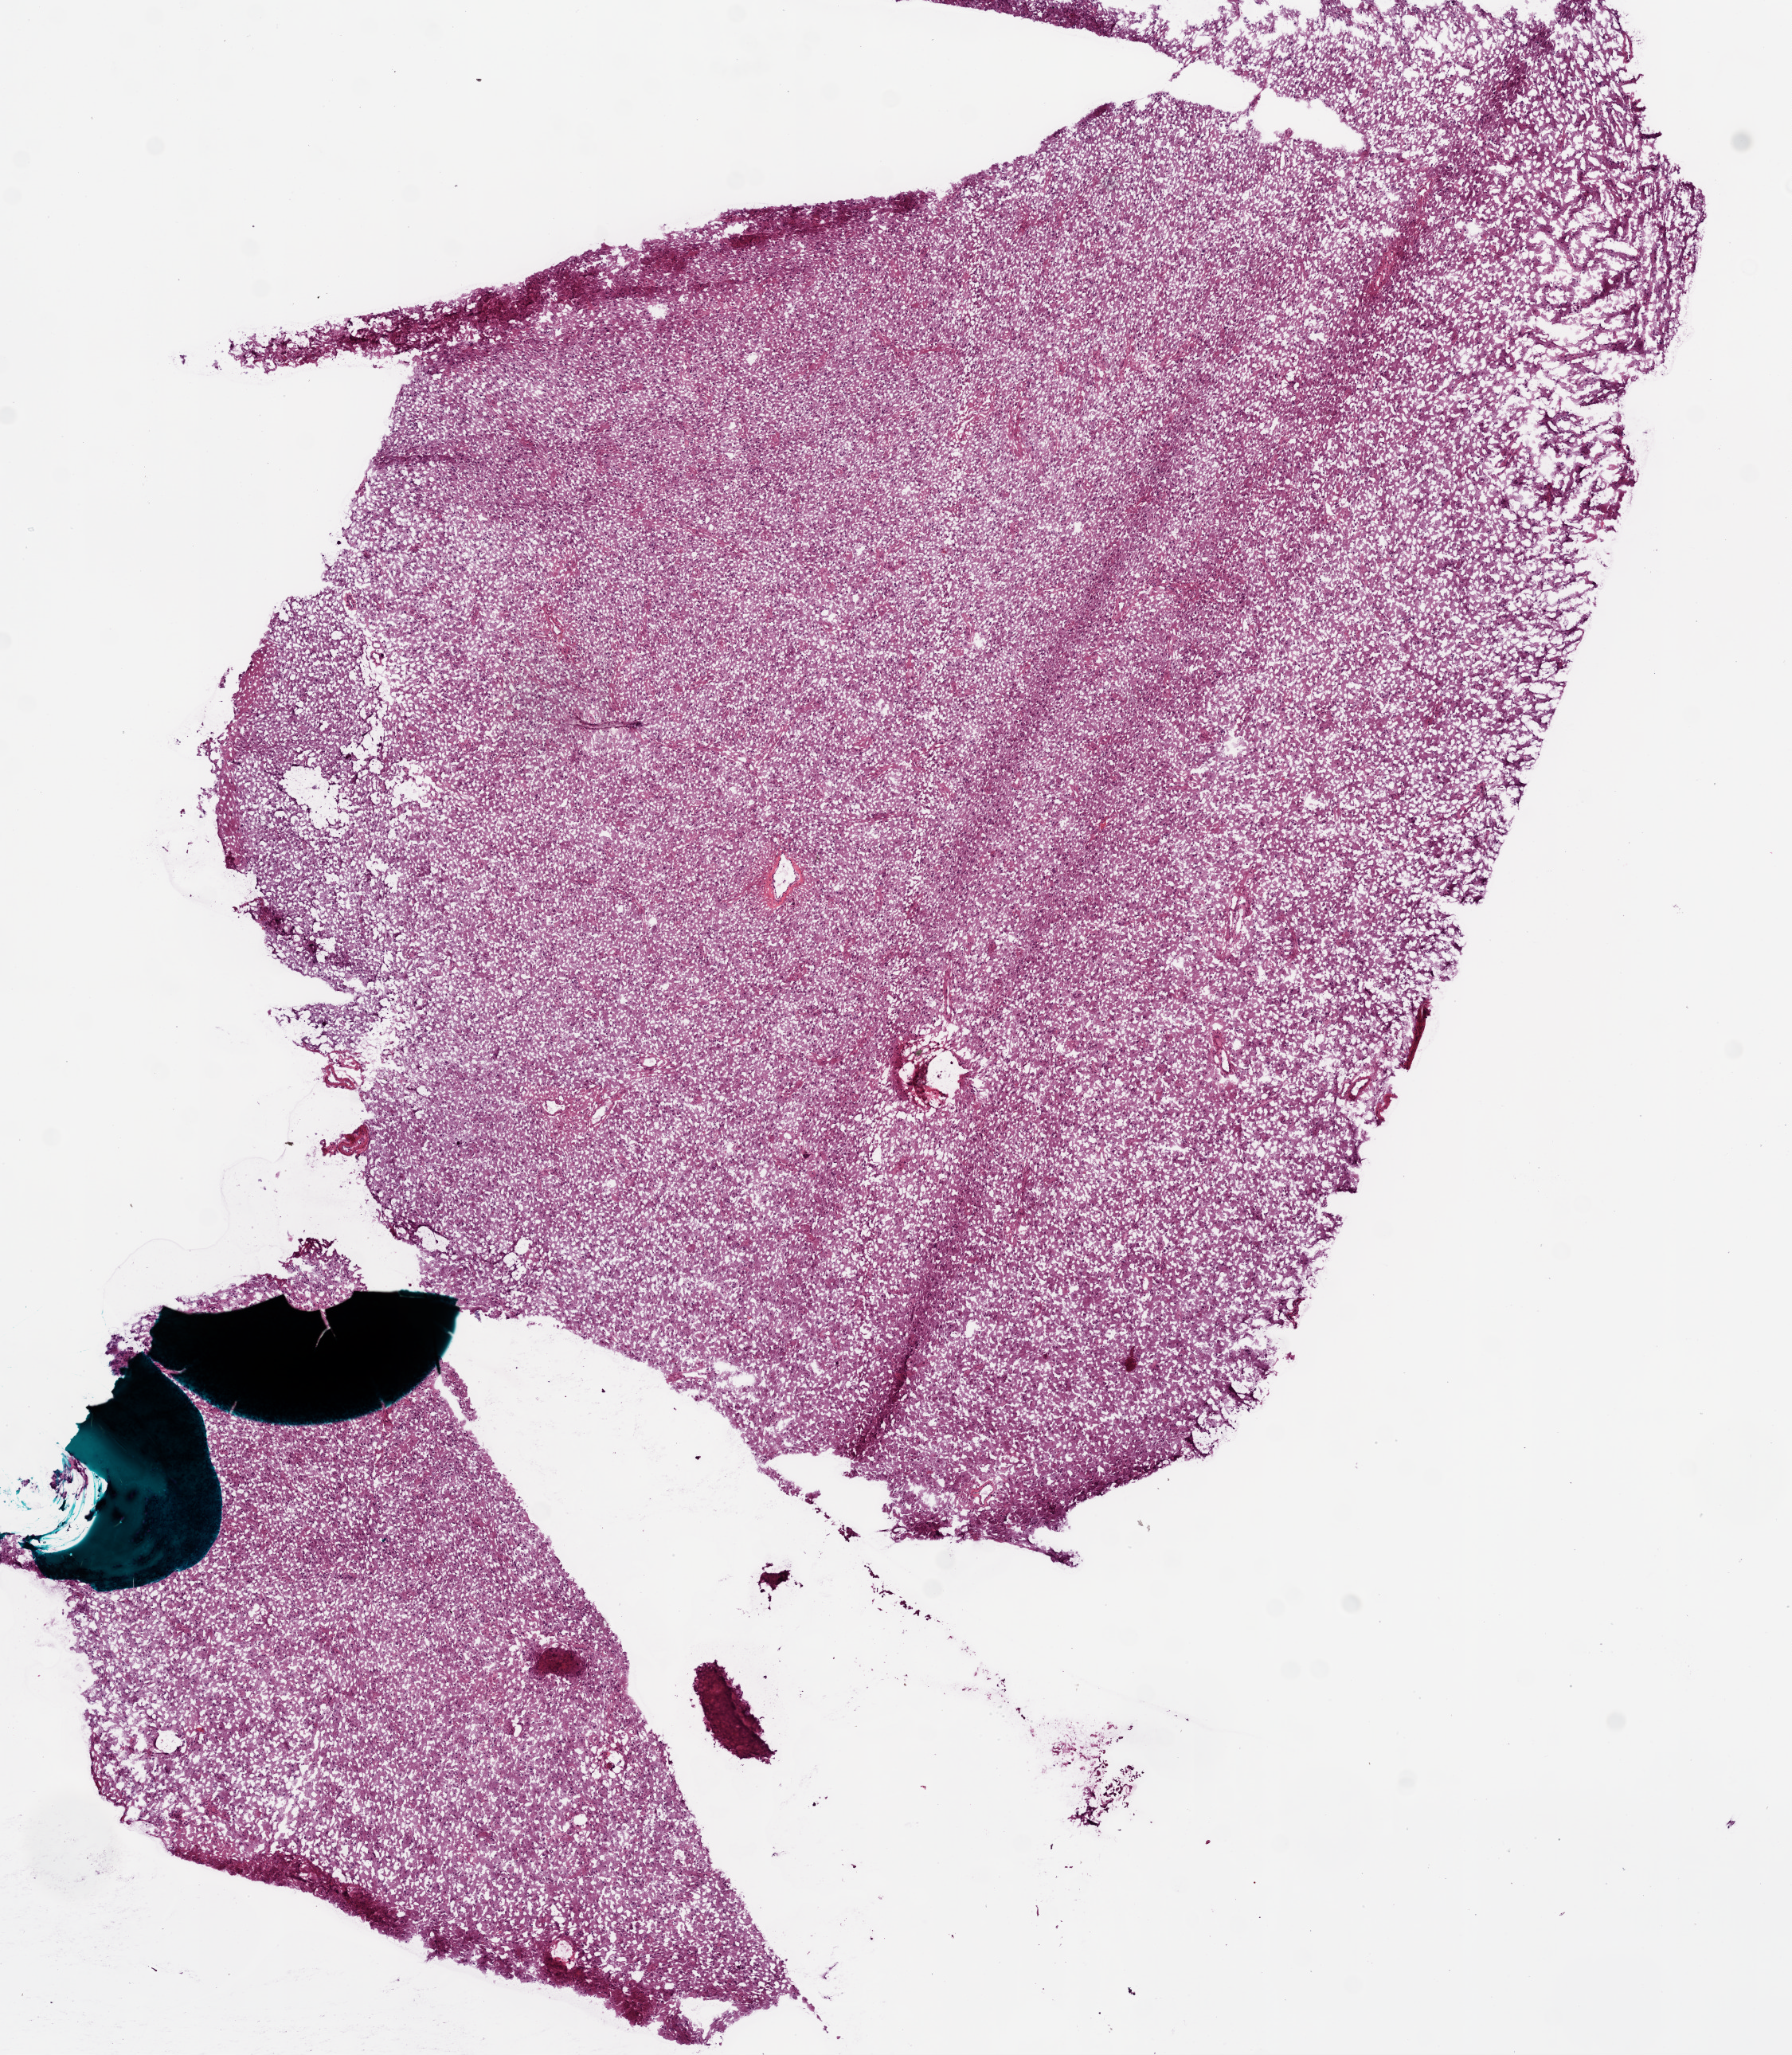
Digitized H&E tissue section (whole slide), whole scanned area (about 9.0 x 10.4 mm) shown as a low-resolution overview. Frozen section from the bottom of the tissue portion. Brain, primary tumour sample. Male patient; age at initial diagnosis 43 years. Slide review estimates, as recorded: tumour cells 70%, tumour nuclei 65%, normal cells 10%, stromal cells 20%, necrosis 0%.
Histologic diagnosis: Glioblastoma.